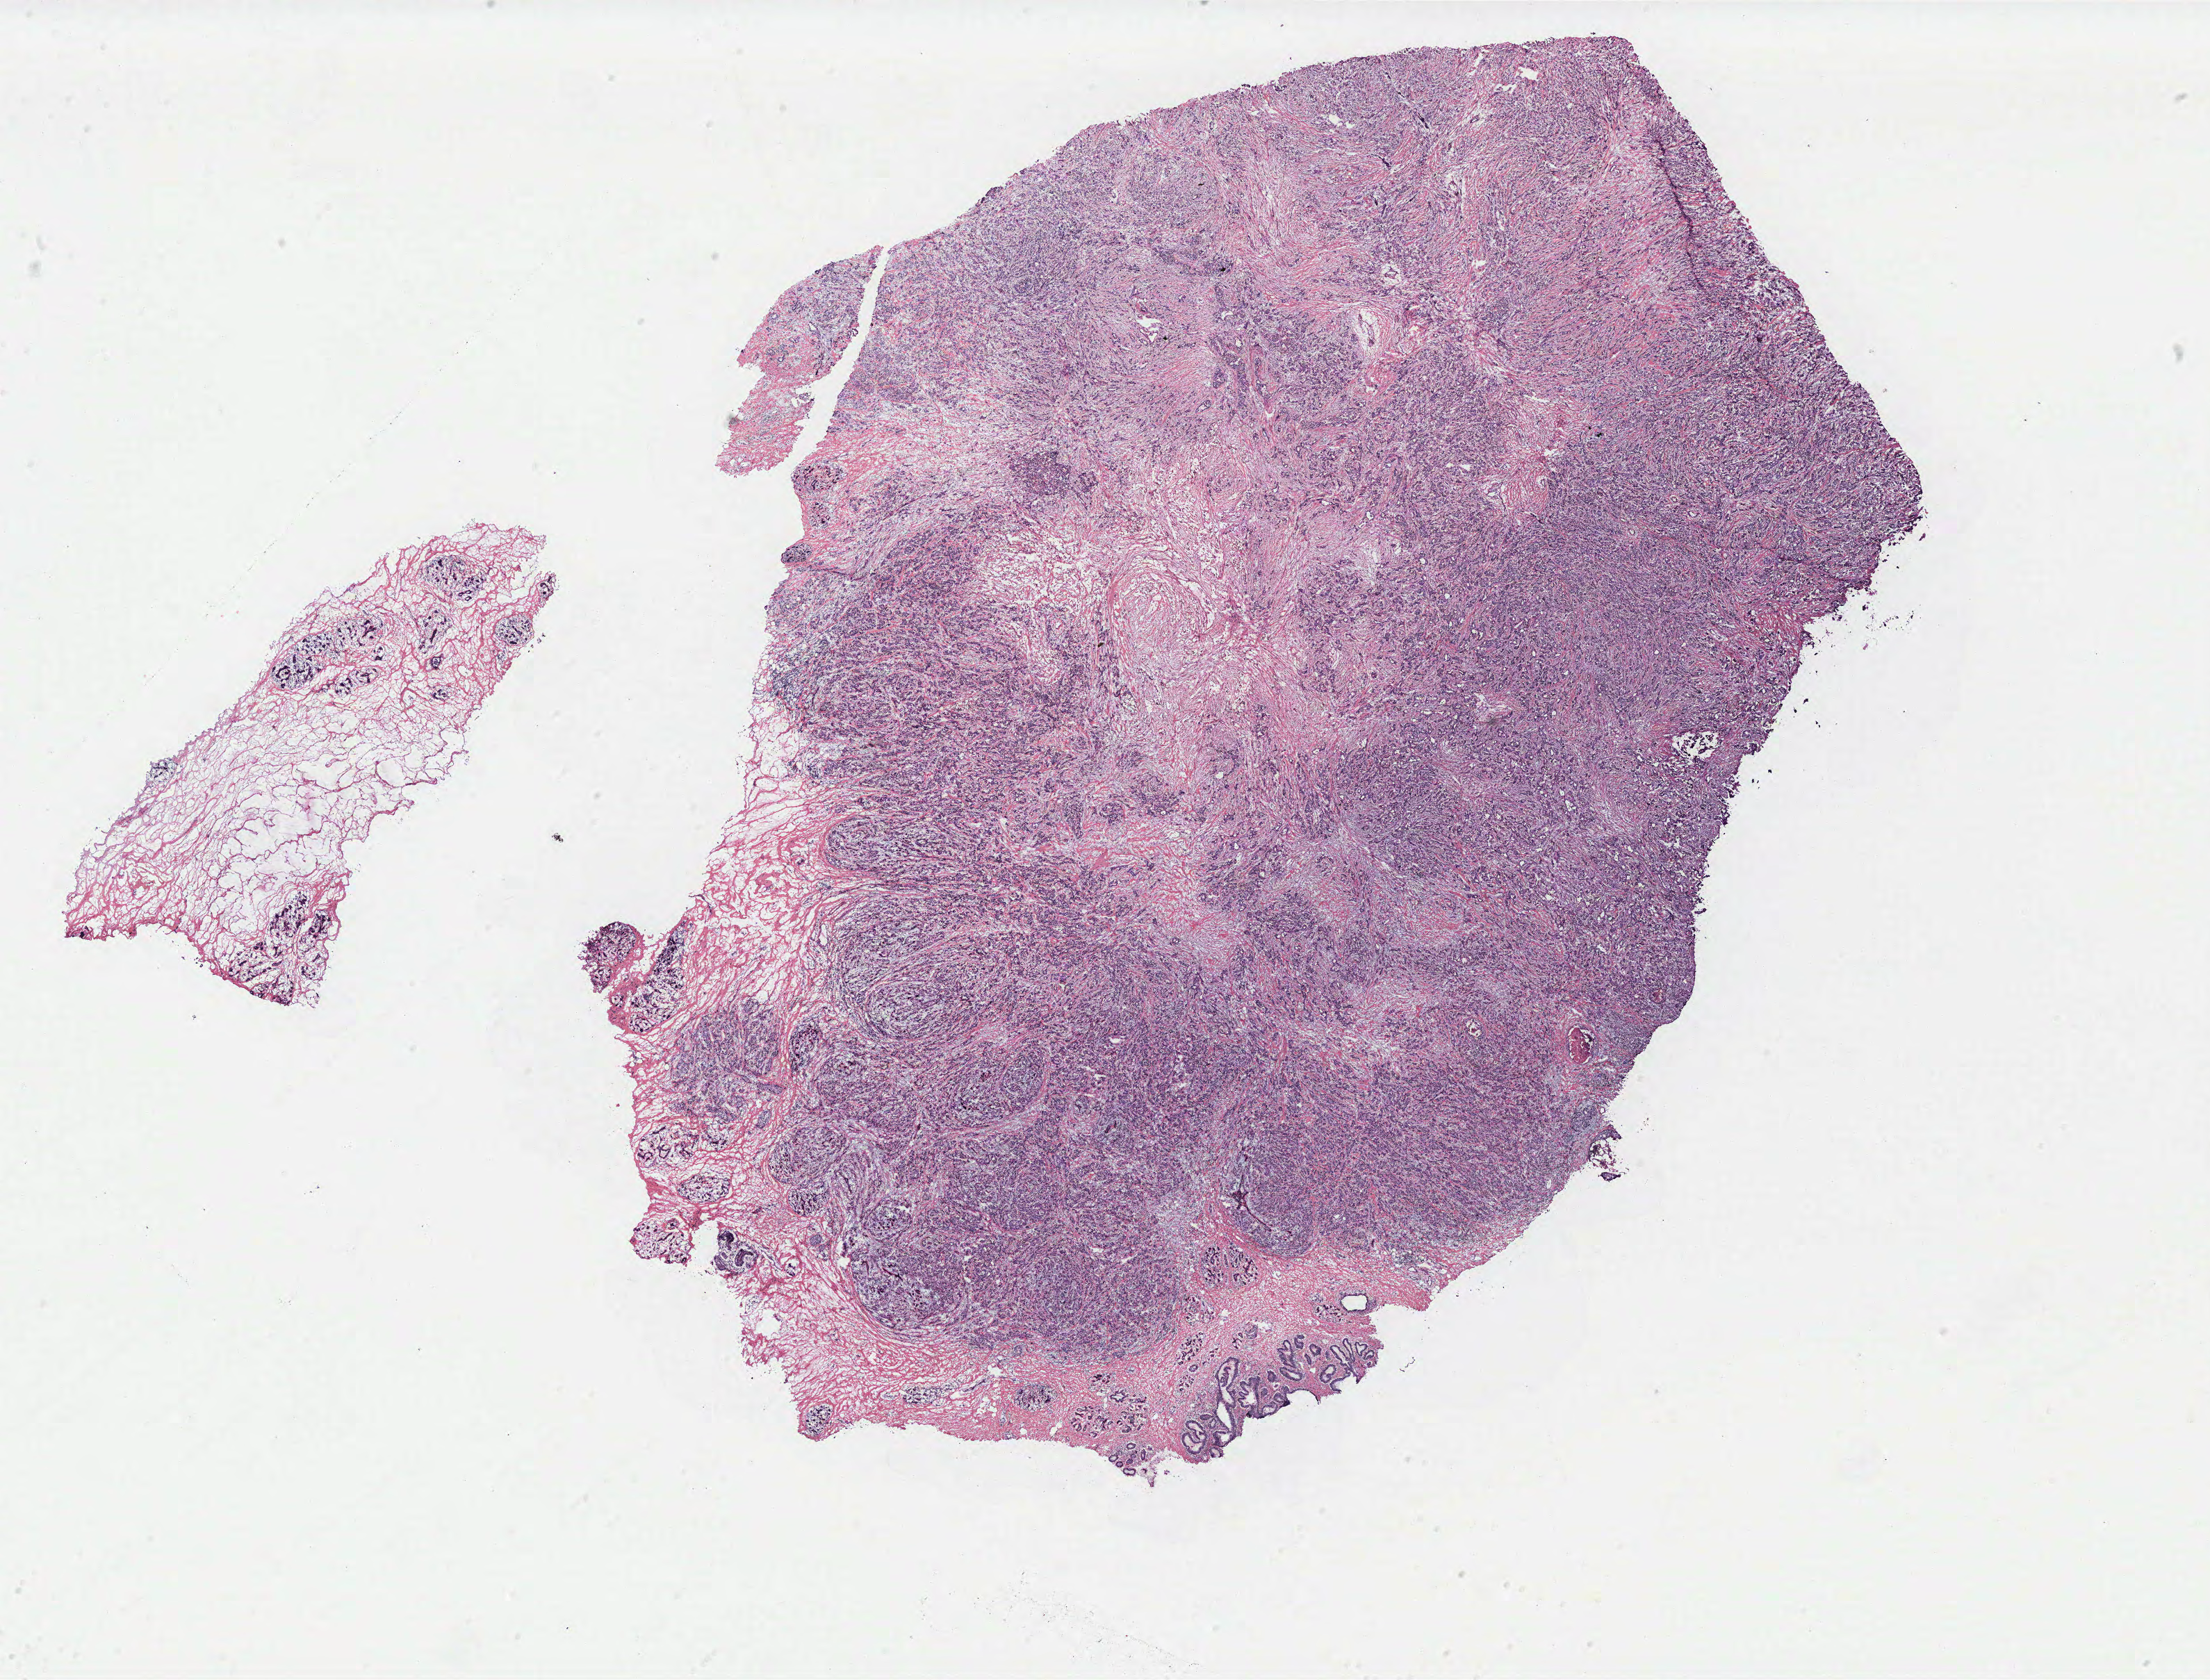
Digitized H&E tissue section (whole slide), low-resolution overview of the scanned area, about 25.5 x 19.4 mm, breast, tissue type not recorded. Patient: female, age 35 years.
Patient diagnosis: Infiltrating duct carcinoma, NOS.